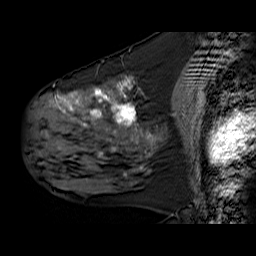
Breast MRI (dynamic contrast-enhanced), one sagittal slice; slice 30 of 60 in the series (ordered by position); dynamic contrast-enhanced series, time point 2 of 6 at this slice position (early post-contrast); 1.5 T; TE 6.3 ms, TR 32.9 ms; 4 mm slice thickness; 256 × 256 image matrix. Female patient. From the clinical record (not read from this slice): setting: breast cancer imaged before/during neoadjuvant chemotherapy; receptor status: HER2-positive.
Outlined on this slice (semi-automatic segmentation, software-assisted and operator-edited):
- analysis volume of interest (the breast-tissue region the enhancement analysis was run in; not a lesion): bounding box [x1, y1, x2, y2] px = [30, 78, 158, 180]
- tumour enhancement mask (voxels above the 100 % enhancement threshold inside the analysis volume of interest): [54, 78, 142, 169]